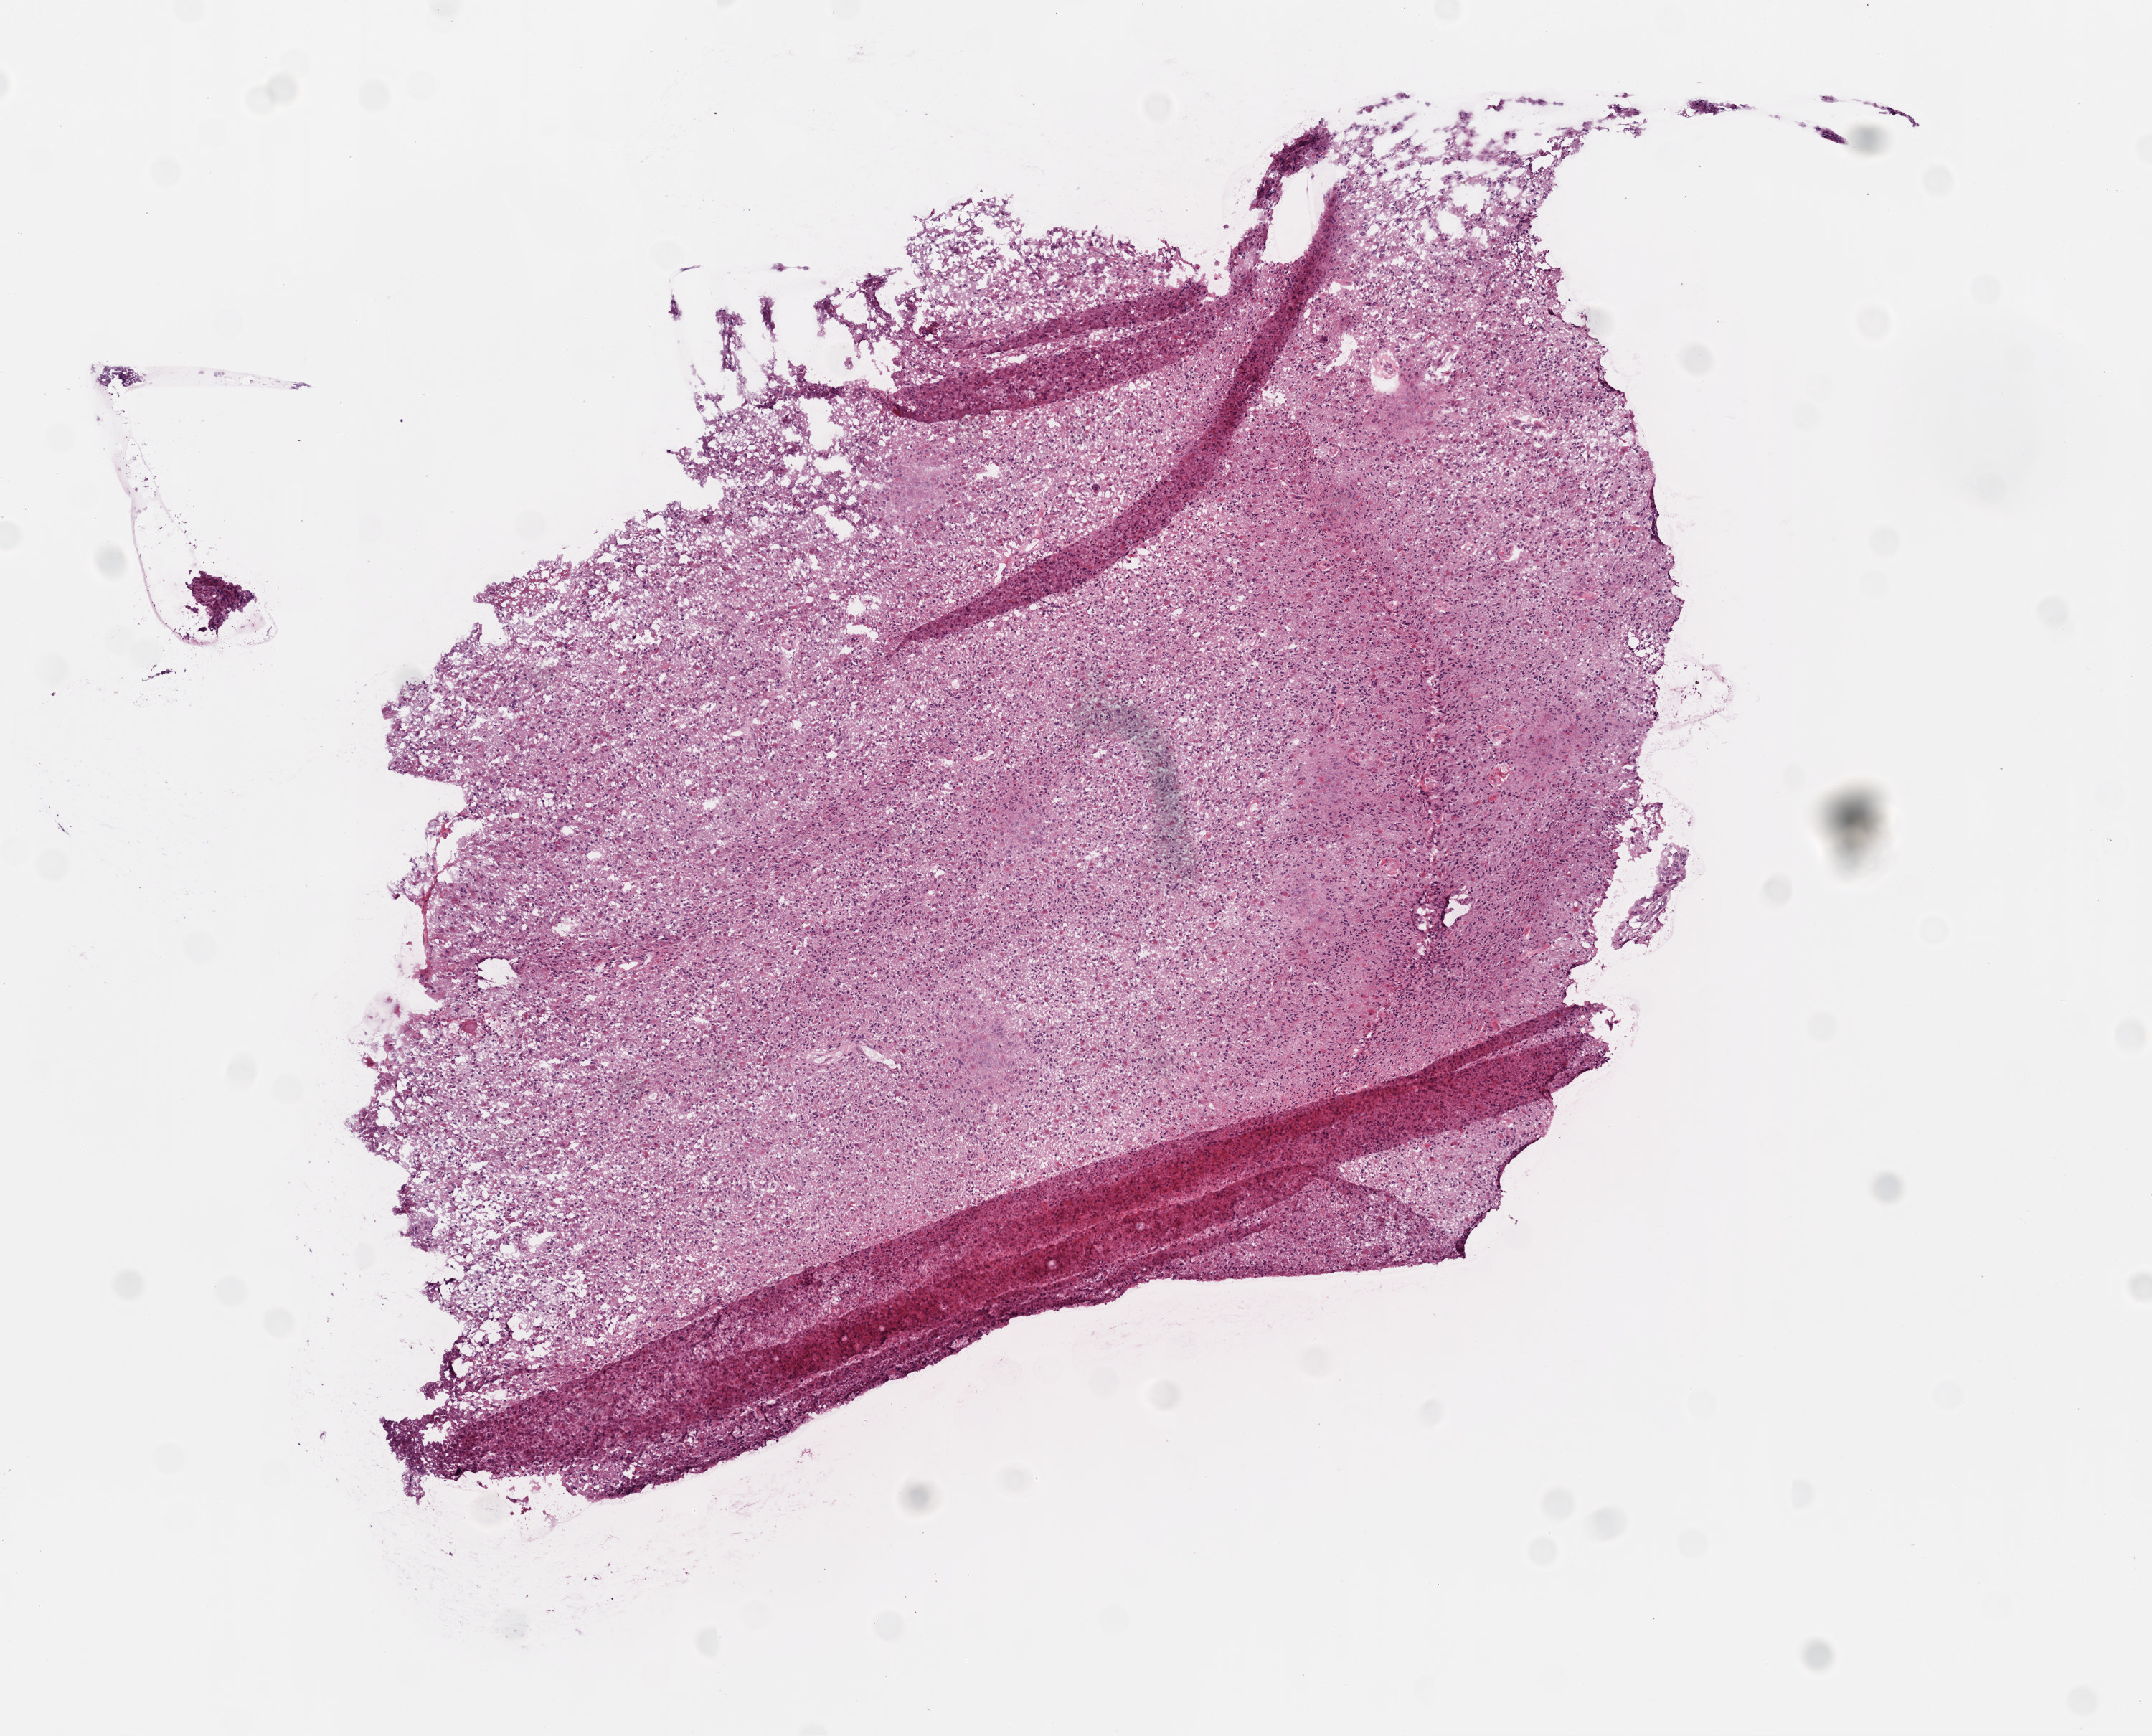
Hematoxylin and eosin (H&E) stained whole-slide image — whole scanned area (about 6.0 x 4.9 mm, acquisition: 20x scan) shown as a low-resolution overview; frozen section; primary tumour sample from the brain. Female patient; age at initial diagnosis 59 years. Pathologist review of this section (percent, as recorded): tumour cells 85%, tumour nuclei 90%, normal cells 0%, stromal cells 5%, necrosis 10%.
Histologic diagnosis: Glioblastoma.